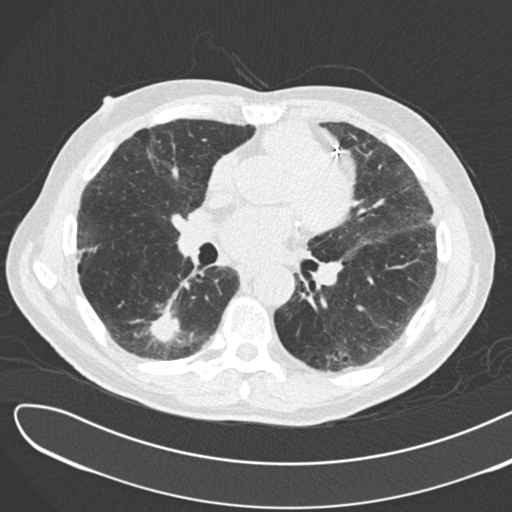
Low-dose screening chest CT, one axial slice. Slice 87 of 183 in the series (ordered by position). Lung window (W 1500 / L -600 HU). 2 mm slice thickness. 512 × 512 image matrix, field of view 370 × 370 mm.
Outlined on this slice (expert manual segmentation):
- lesion 1 (tumor, lower lobe of right lung): bounding box <150,301,182,345> (left, top, right, bottom; pixels)